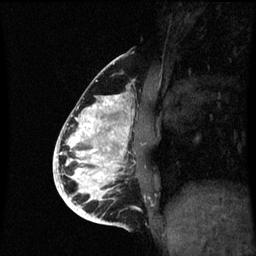
Breast MRI (dynamic contrast-enhanced), one sagittal slice; position 28 of 60 along the scan axis; dynamic contrast-enhanced series, image 2 of 3 at this slice position (ordered by acquisition); 1.5 T; TE 4.2 ms, TR 8.9 ms; 2 mm slice thickness; 256 × 256 image matrix, field of view 200 × 200 mm. Female patient, age 35 years. Case-level facts recorded for this patient, not image findings: setting: breast cancer imaged before/during neoadjuvant chemotherapy; receptor status: HR-positive, HER2-negative.
Outlined on this slice (semi-automatically segmented with operator editing):
- analysis volume of interest (the breast-tissue region the enhancement analysis was run in; not a lesion): box from (x=66, y=94) to (x=140, y=215) px
- tumour enhancement mask (voxels above the 70 % enhancement threshold inside the analysis volume of interest): (x=66, y=94)–(x=130, y=215)